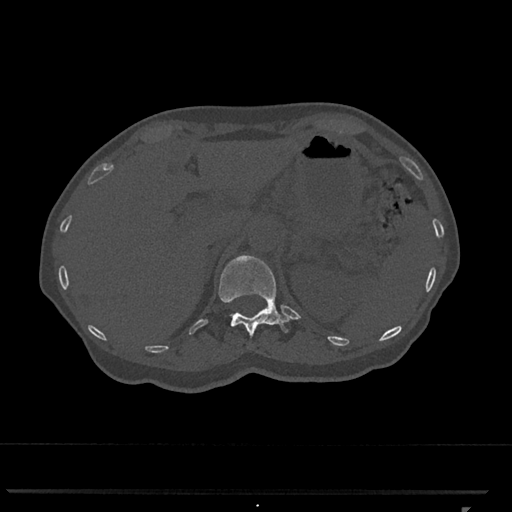
CT including the spine, one axial slice. Slice 457 of 793 in the series (ordered by position). Reconstruction kernel Br40s/3. 120 kVp. Bone window (W 1800 / L 400 HU). 0.5 mm slice thickness. 512 × 512 image matrix. Female patient, age 62 years. From the clinical record (not read from this slice): primary cancer: renal.
Annotated regions visible in this slice (semi-automatic segmentation, software-assisted and operator-edited):
- T12 vertebra: bounding box (x1, y1, x2, y2) in pixels: (219, 255, 291, 337)